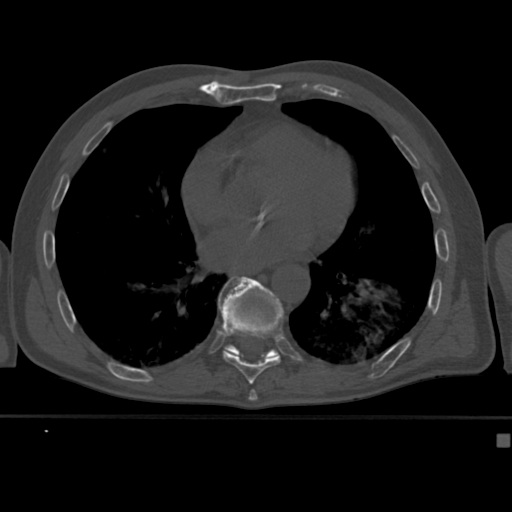
CT including the spine, one axial slice. Position 242 of 430 along the scan axis. 120 kVp. Bone window (W 1800 / L 400 HU). 1.5 mm slice thickness. 512 × 512 image matrix, field of view 337 × 337 mm. Male patient, age 64 years. From the clinical record (not read from this slice): primary cancer: uterus; vertebrae with lytic lesions (as recorded): T1, T4, T5, T7, L5.
Structures marked on this image (semi-automatically segmented with operator editing):
- T10 vertebra: bounding box (x1, y1, x2, y2) in pixels: (224, 277, 284, 361)
- T9 vertebra: (218, 277, 283, 382)